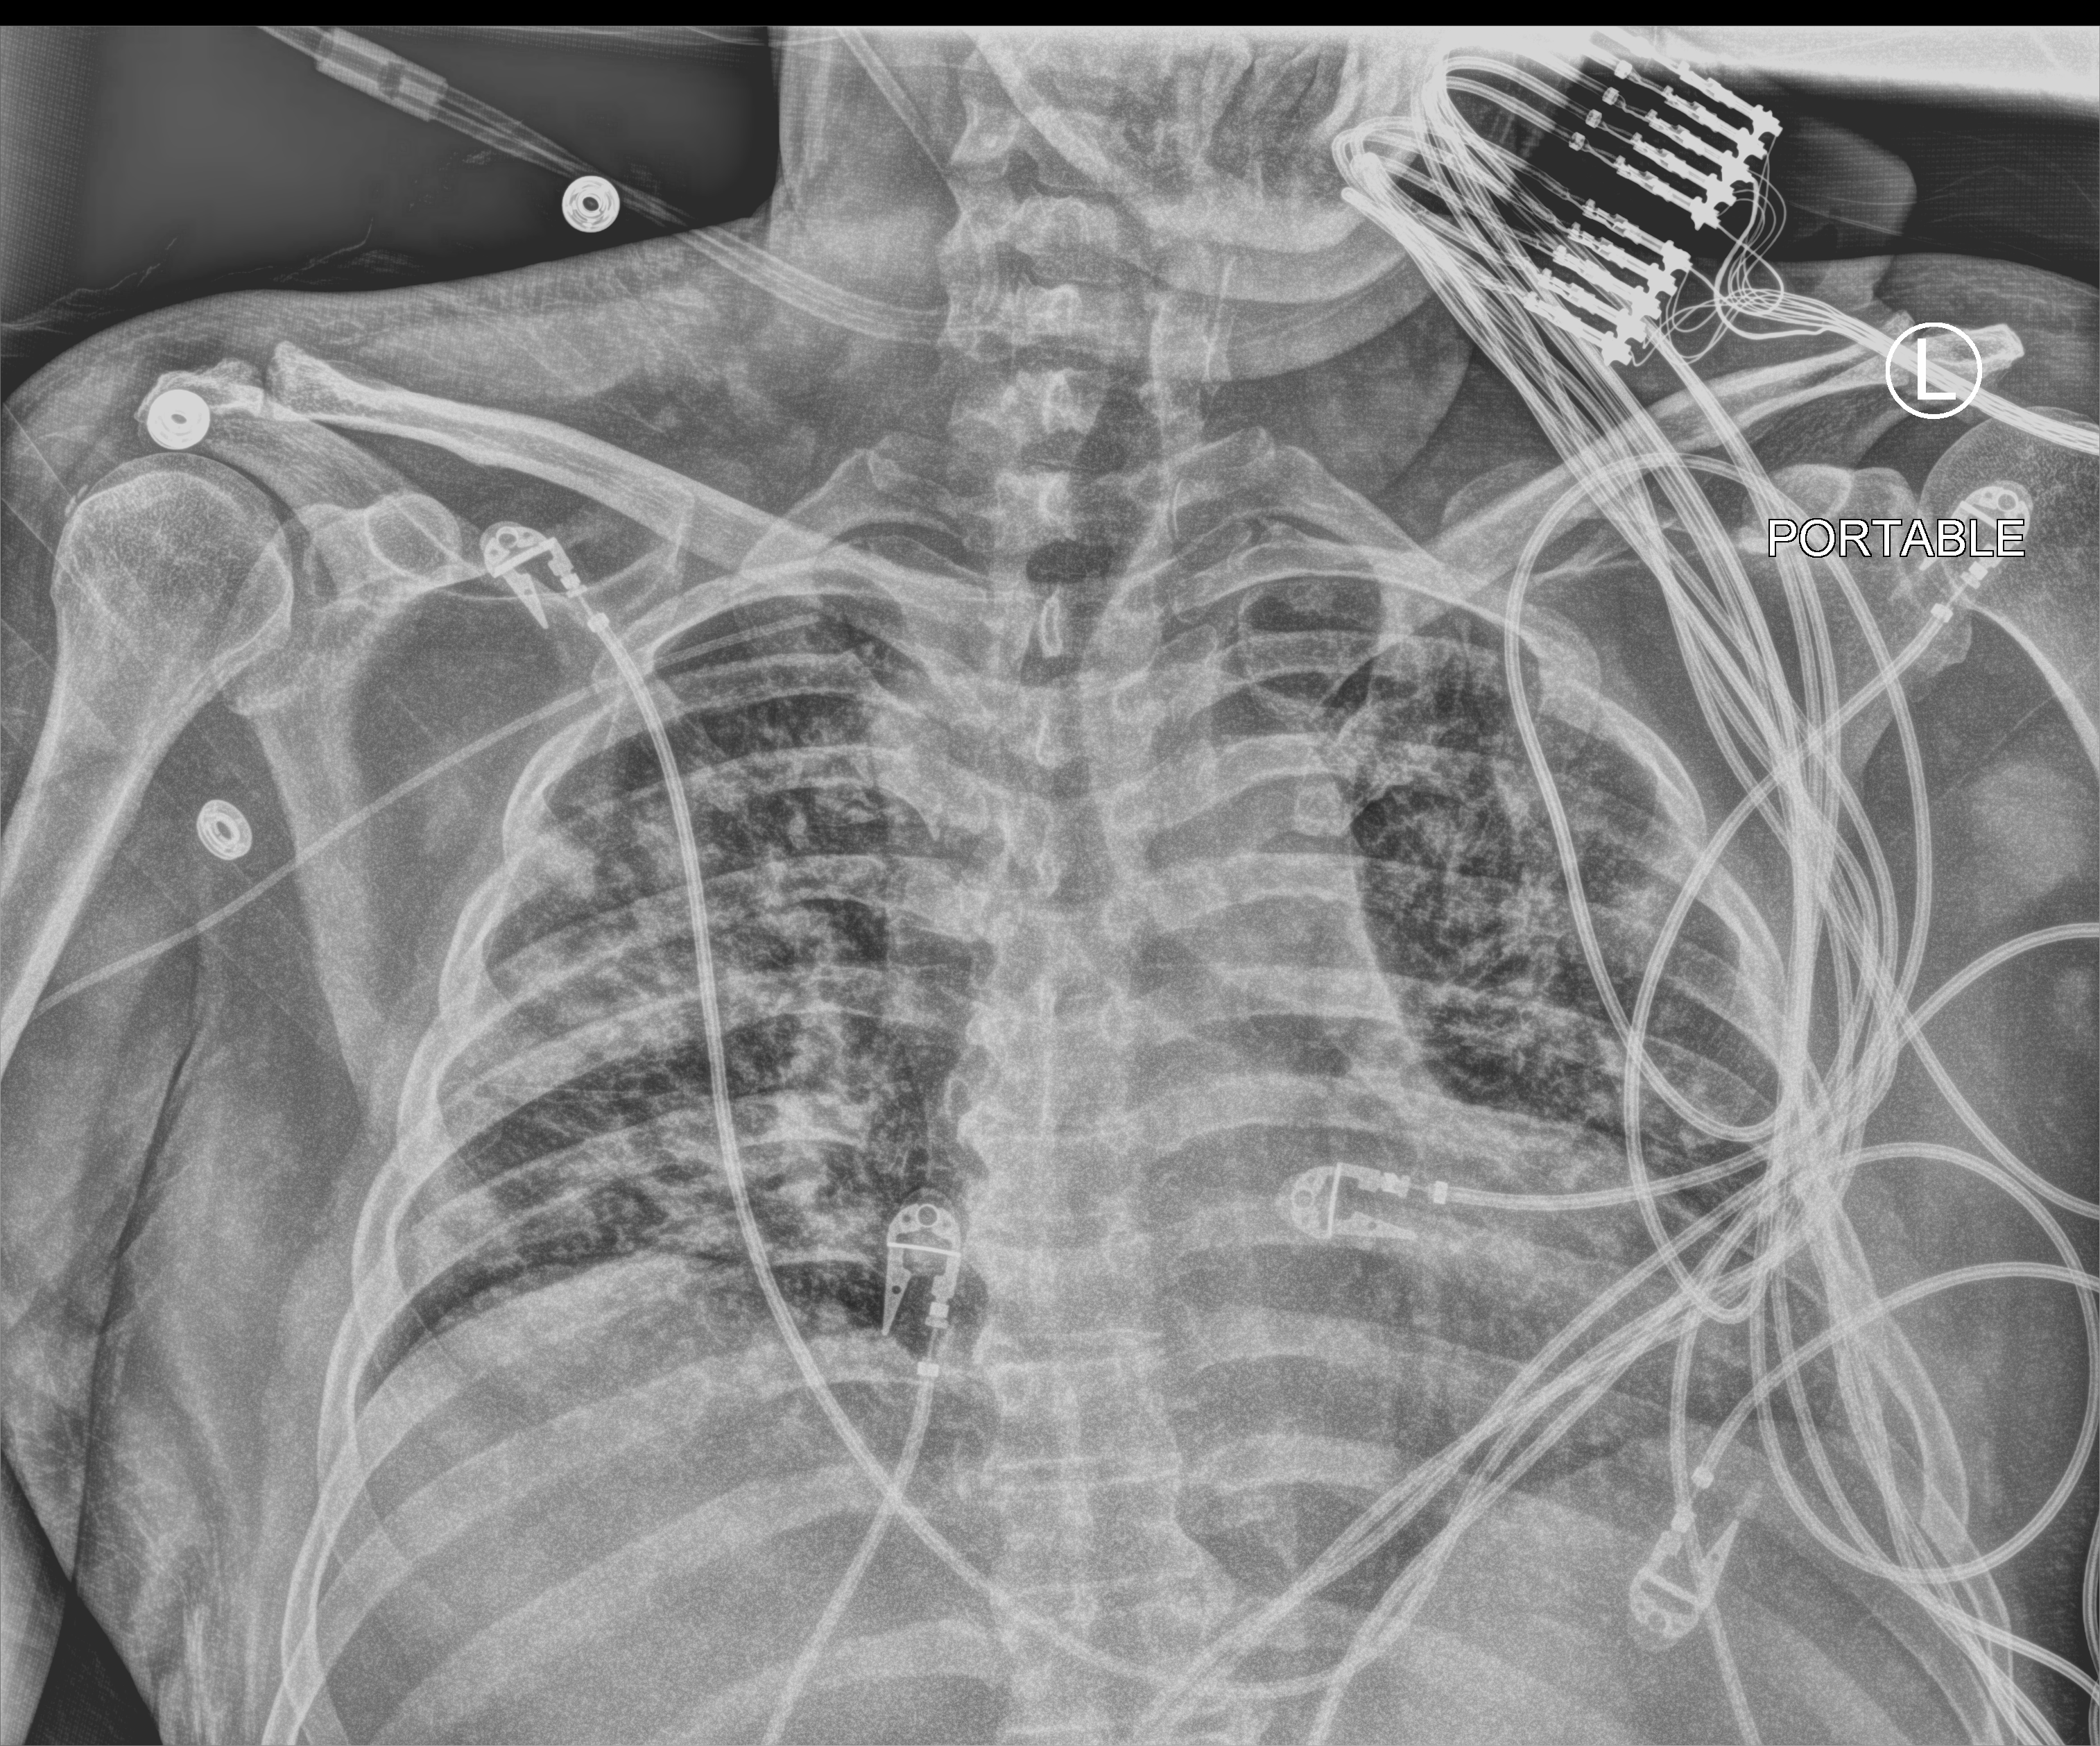
Portable chest radiograph; anteroposterior (AP) projection. Male patient hospitalised with COVID-19, age 18–59 years.
Hospital-stay facts (about this admission, not read from this image; timing relative to this image not recorded):
- admitted to intensive care during this hospital stay: yes